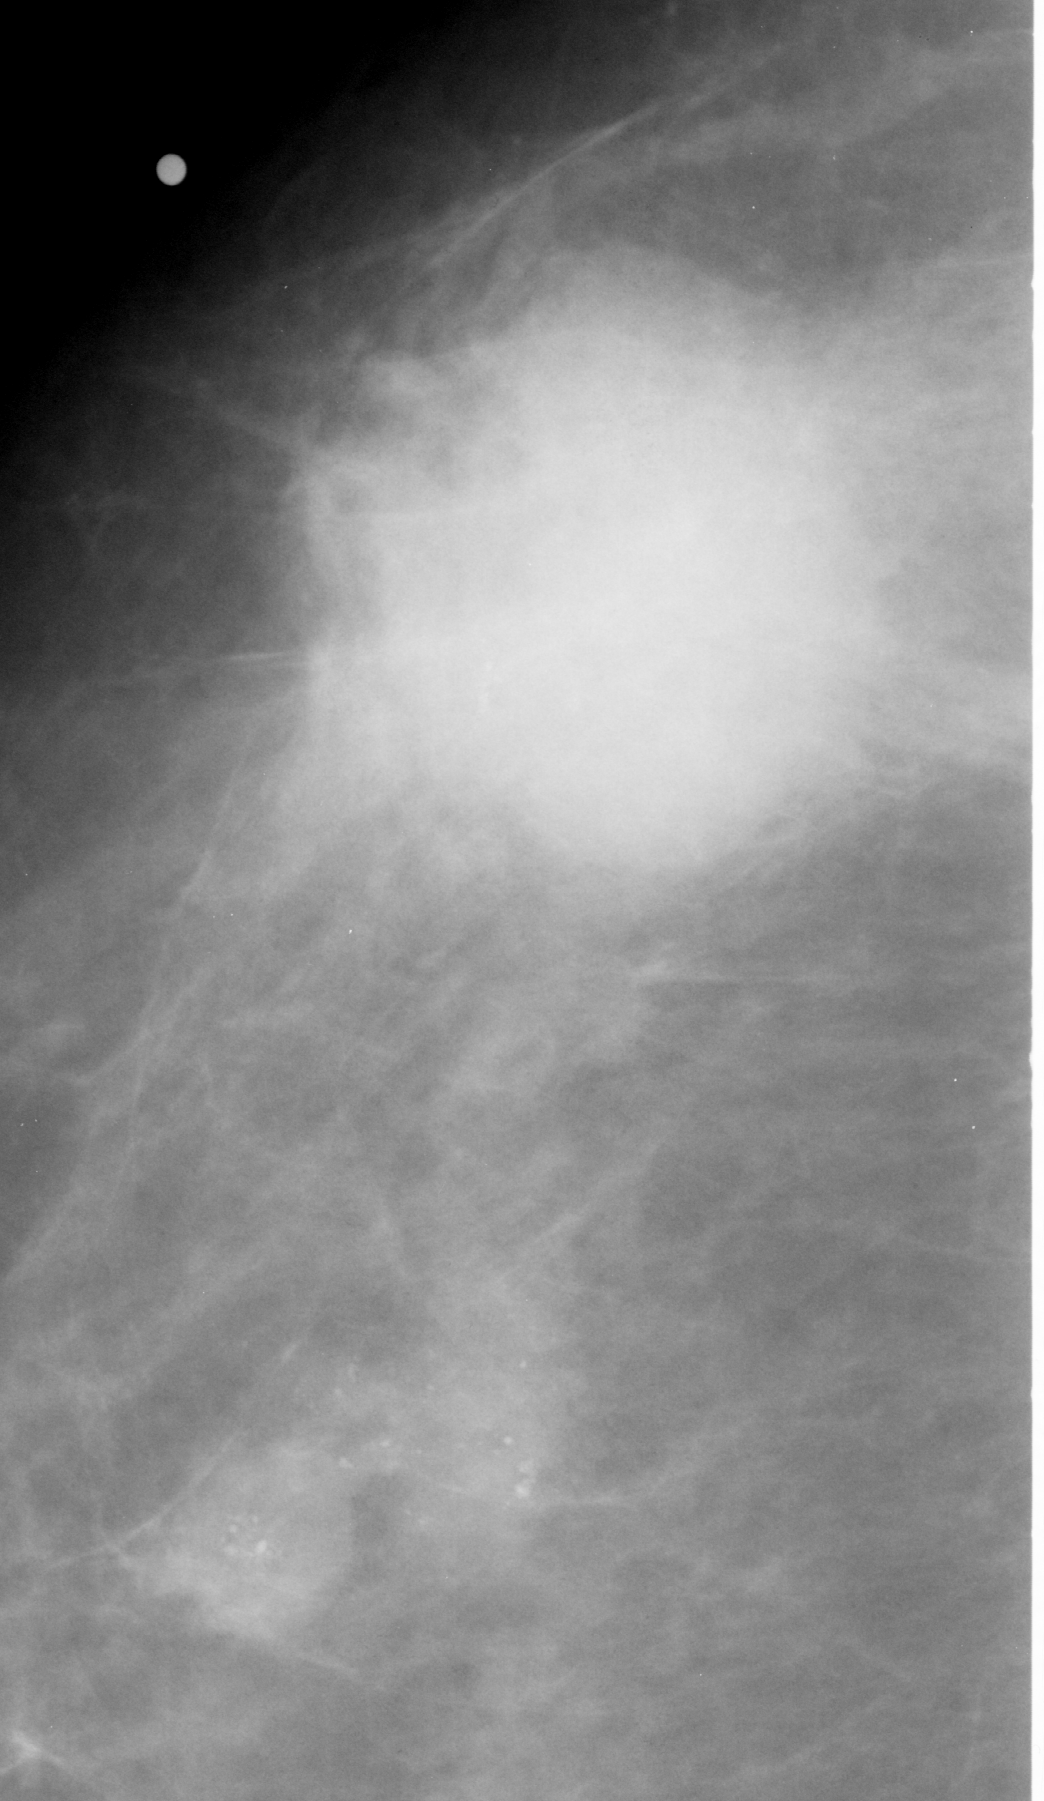
Crop from a digitized film mammogram around one marked abnormality, right breast, CC view.
Finding: calcifications, morphology amorphous, distribution clustered; BI-RADS assessment category 5; subtlety rating 5 on a 1 (subtle) to 5 (obvious) scale; pathology result (as recorded, not read from the image): malignant.